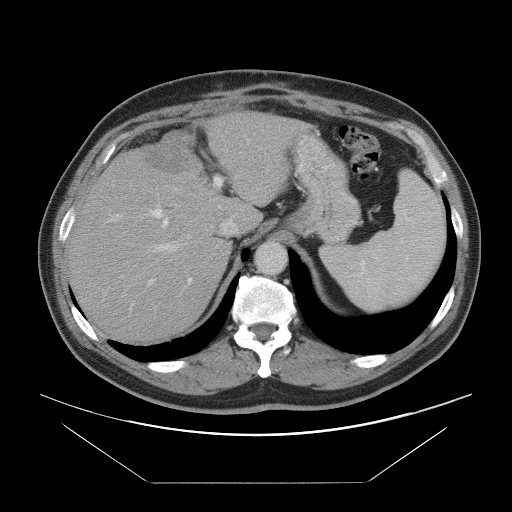
Contrast-enhanced abdominal CT, one axial slice. Position 66 of 97 along the scan axis. 120 kVp. Intravenous contrast given. Soft-tissue window (W 400 / L 40 HU). 512 × 512 image matrix, field of view 442 × 442 mm. Male patient, age 62 years. Case-level facts recorded for this patient, not image findings: diagnosis: colorectal cancer liver metastases, imaged before liver resection; multiple liver metastases: no; largest metastasis: 7 cm; disease in both lobes: yes.
Outlined on this slice (expert manual segmentation):
- hepatic veins: bounding box (x1, y1, x2, y2) in pixels: (148, 139, 285, 255)
- liver: (71, 113, 303, 340)
- planned liver remnant (the part of the liver to remain after resection): (71, 171, 233, 339)
- portal vein (with intrahepatic branches): (107, 140, 250, 311)
- liver metastasis: (143, 132, 191, 173)